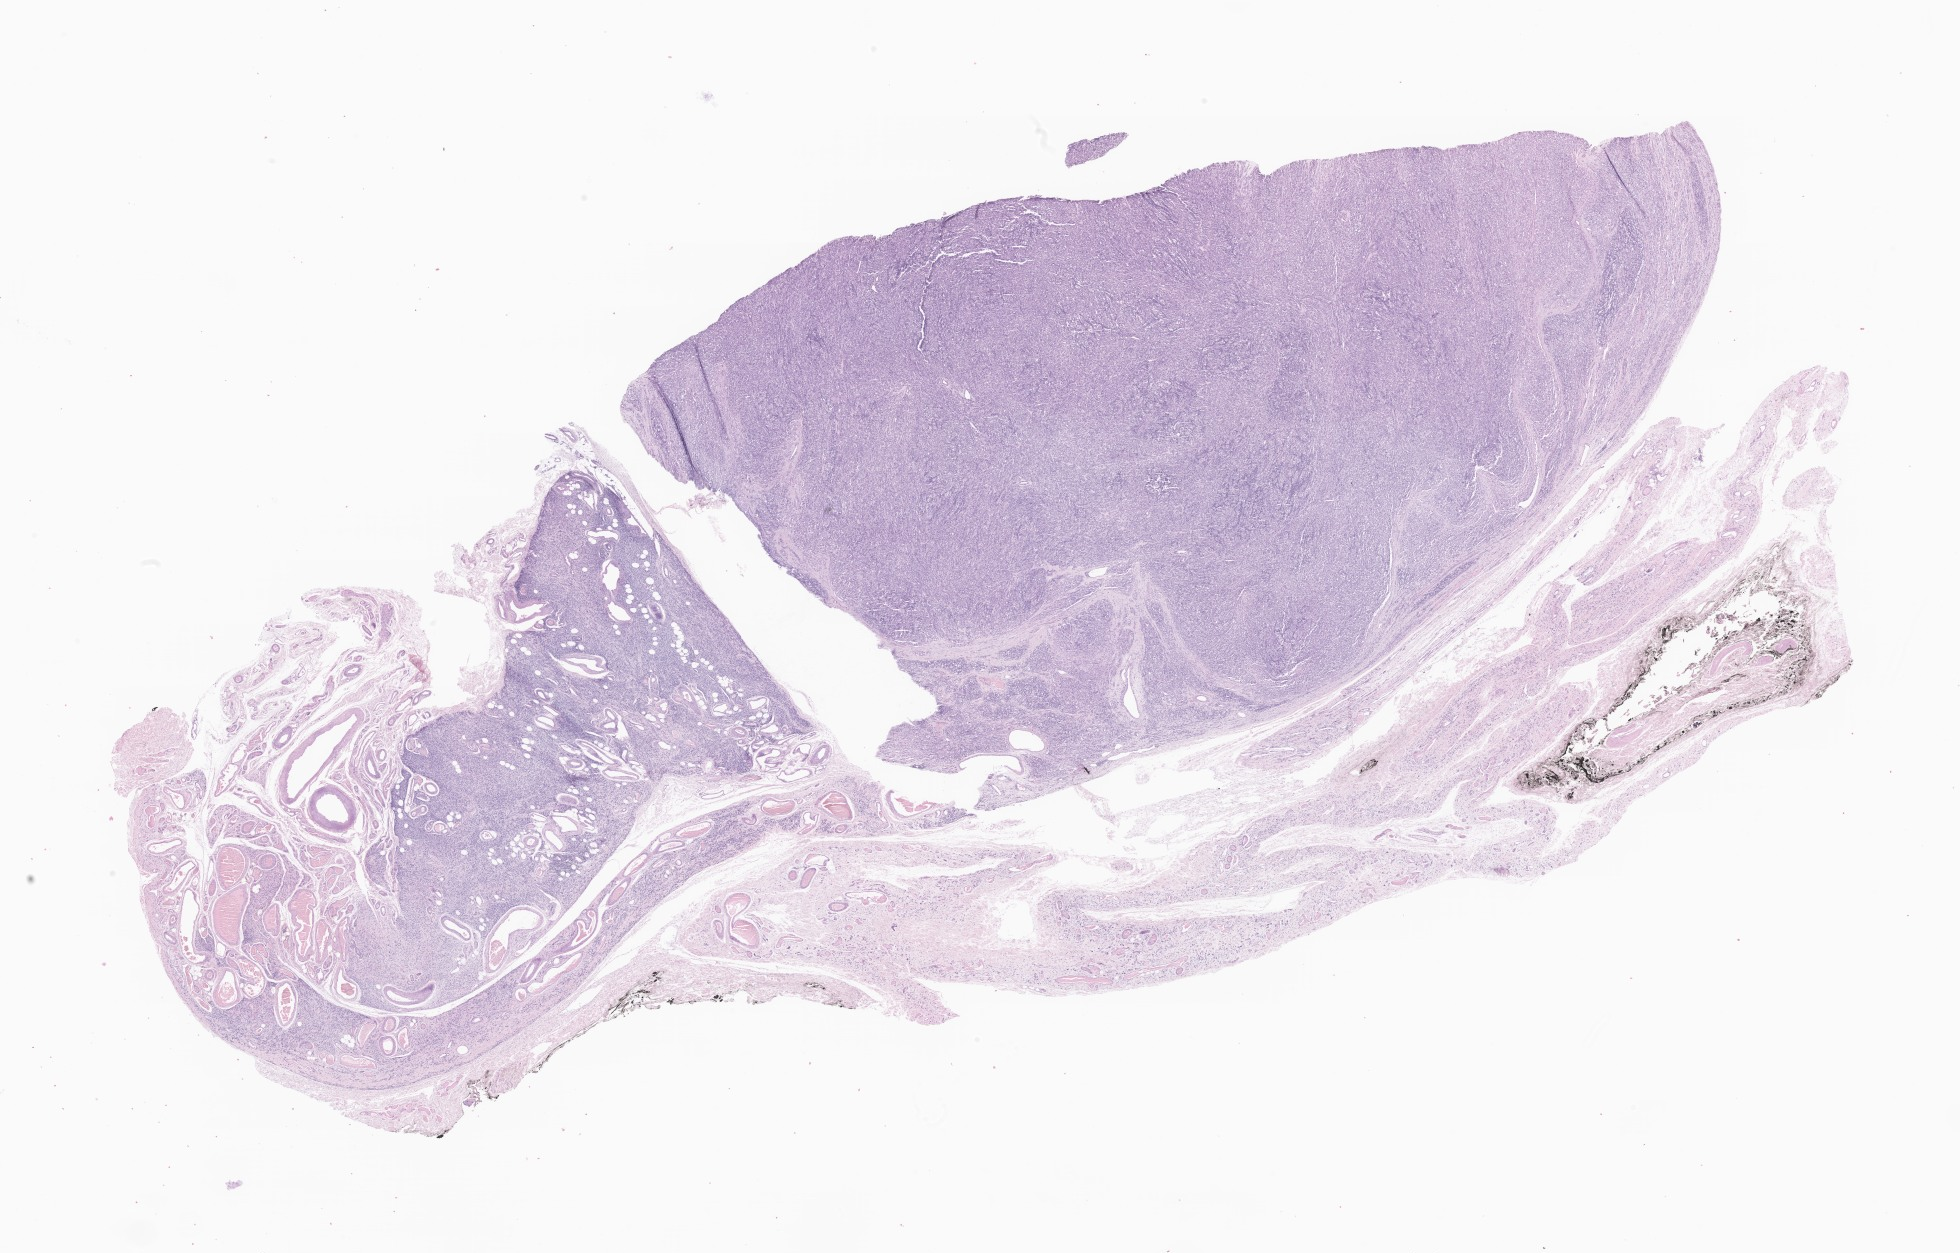
Digitized haematoxylin and eosin-stained section of tumor tissue from the testis — shown as a low-resolution overview of the whole scanned area (about 33.1 x 21.1 mm), formalin-fixed paraffin-embedded section. Patient: male, age 218 months (18 years 2 months).
Diagnosis: Embryonal rhabdomyosarcoma, NOS.